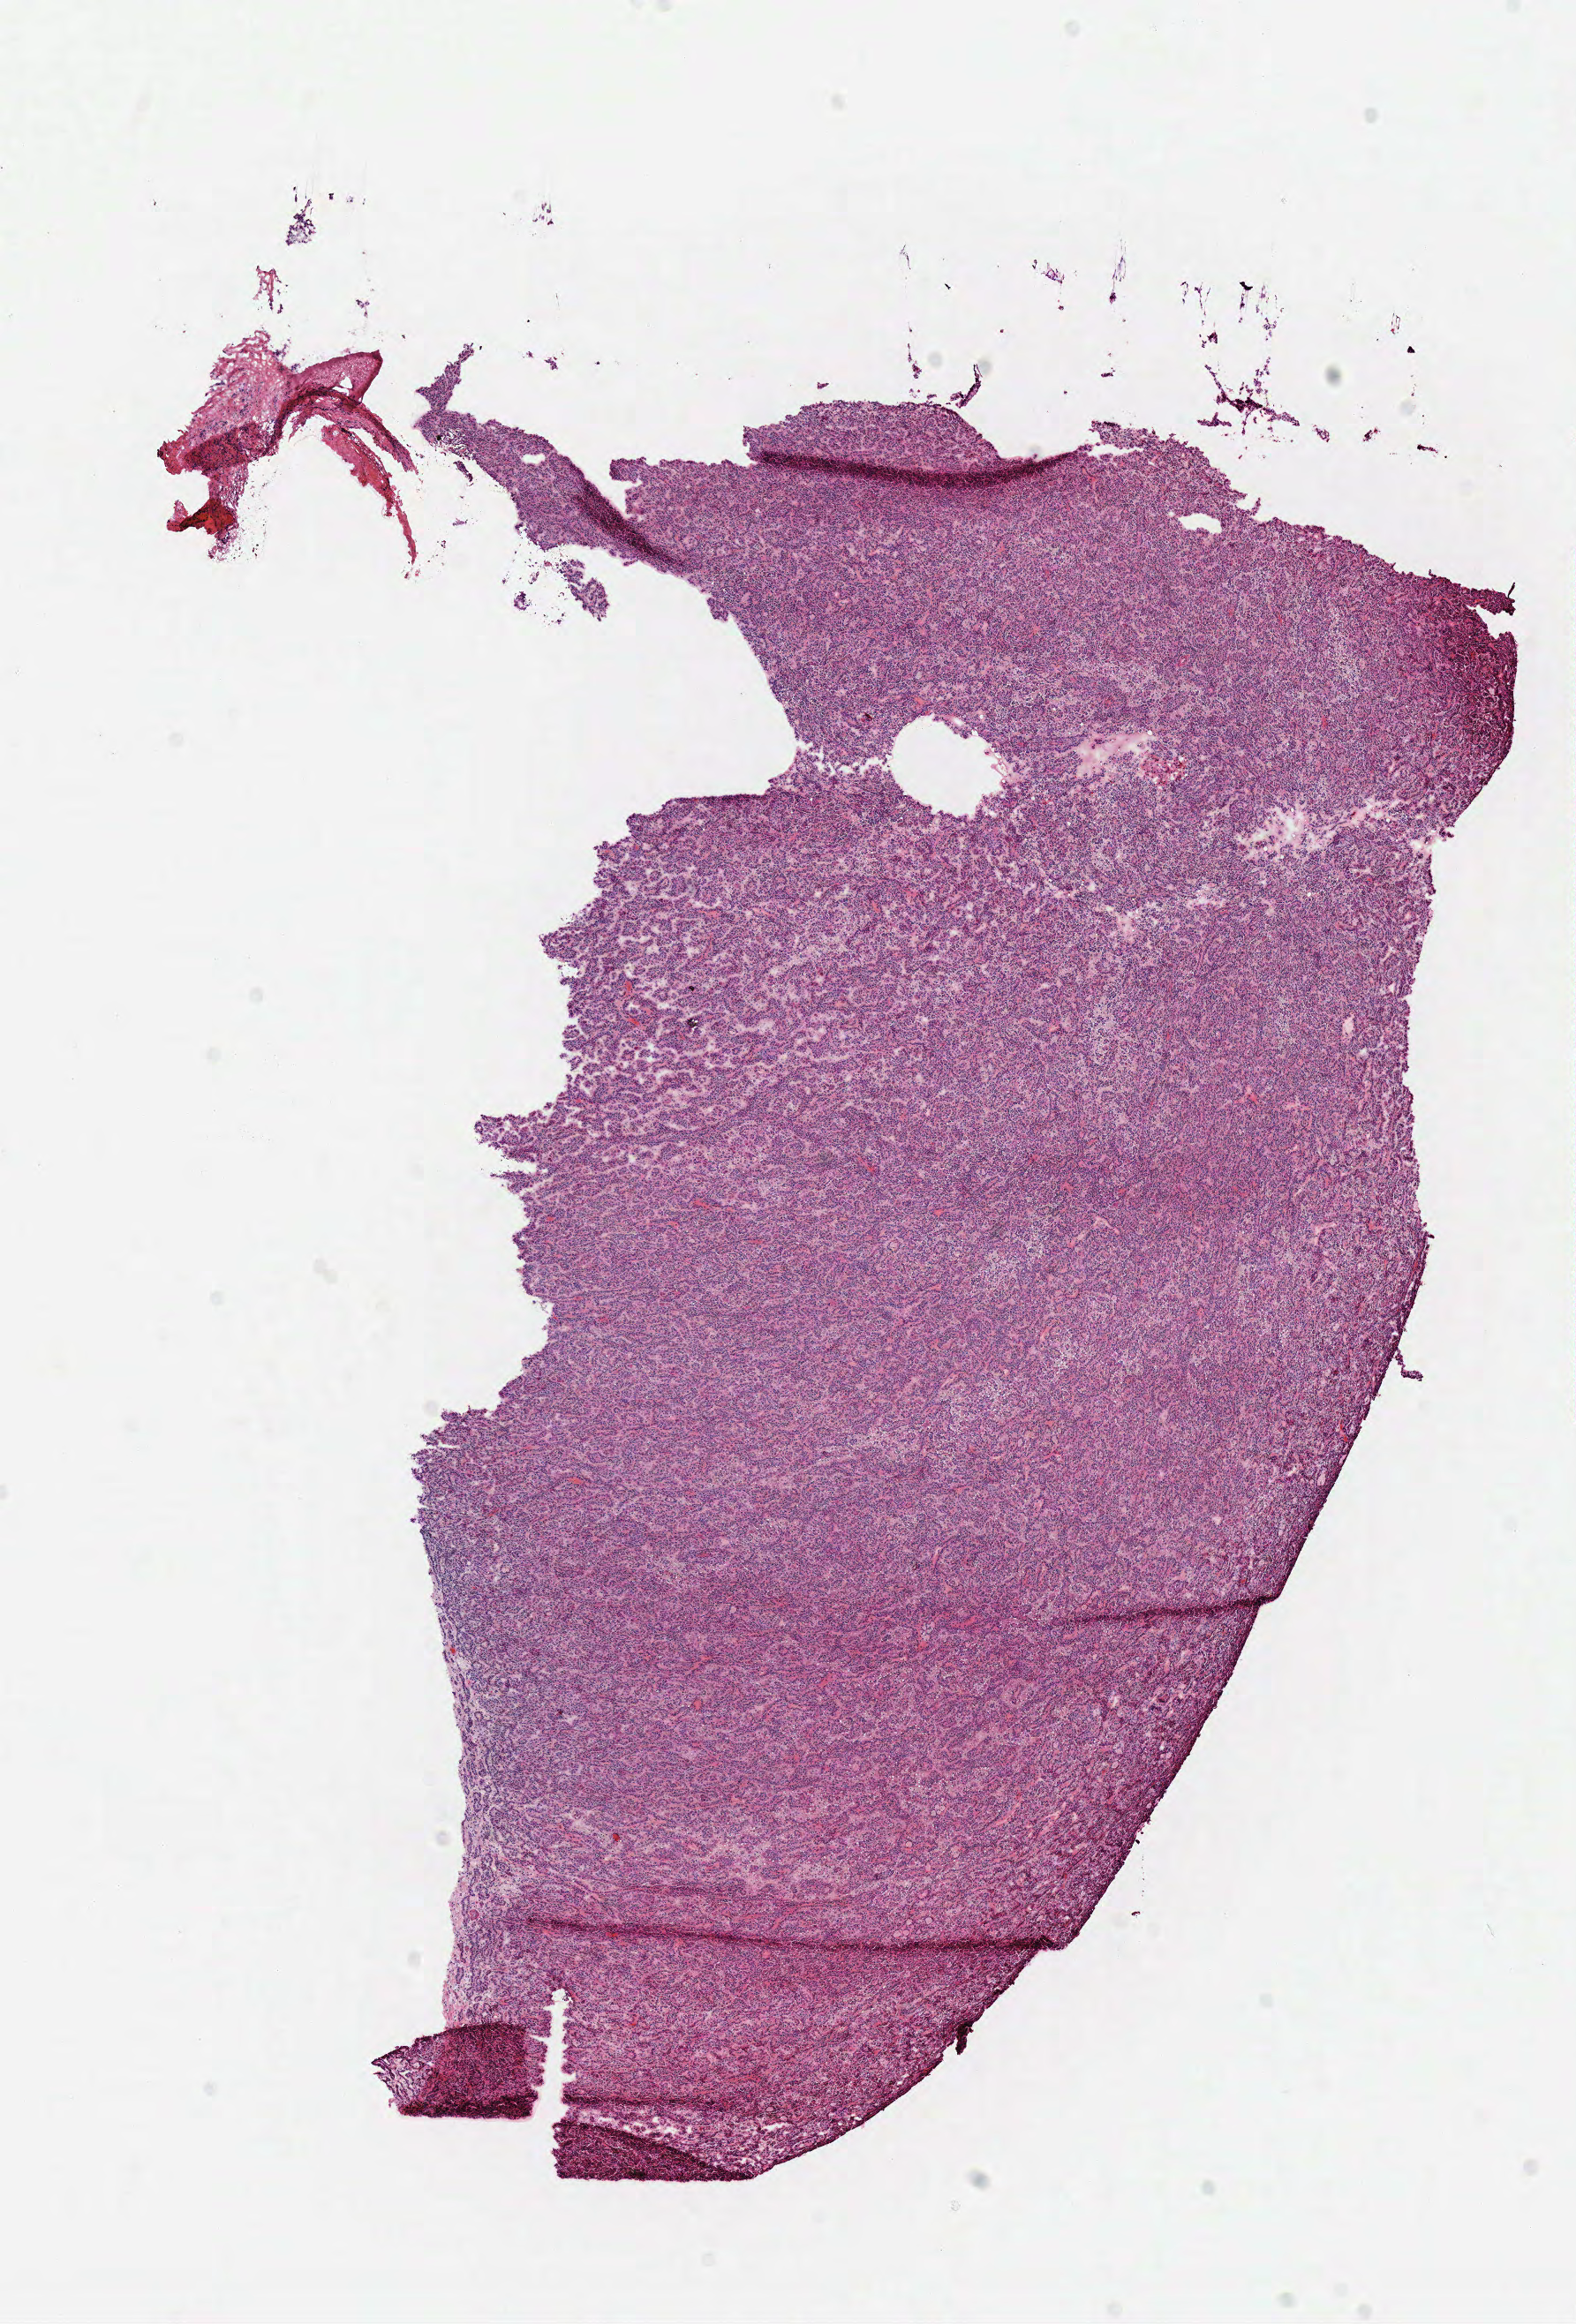
Whole-slide histology image, H&E, whole scanned area (about 7.0 x 10.4 mm) shown as a low-resolution overview, frozen section, primary tumour sample from the kidney. Male patient; age at initial diagnosis 45 years. Pathologist review of this section (percent, as recorded): tumour cells 90%, tumour nuclei 85%, normal cells 0%, stromal cells 10%, necrosis 0%.
- AJCC pathologic stage: I (6th edition)
- pathologic diagnosis: Papillary adenocarcinoma, NOS